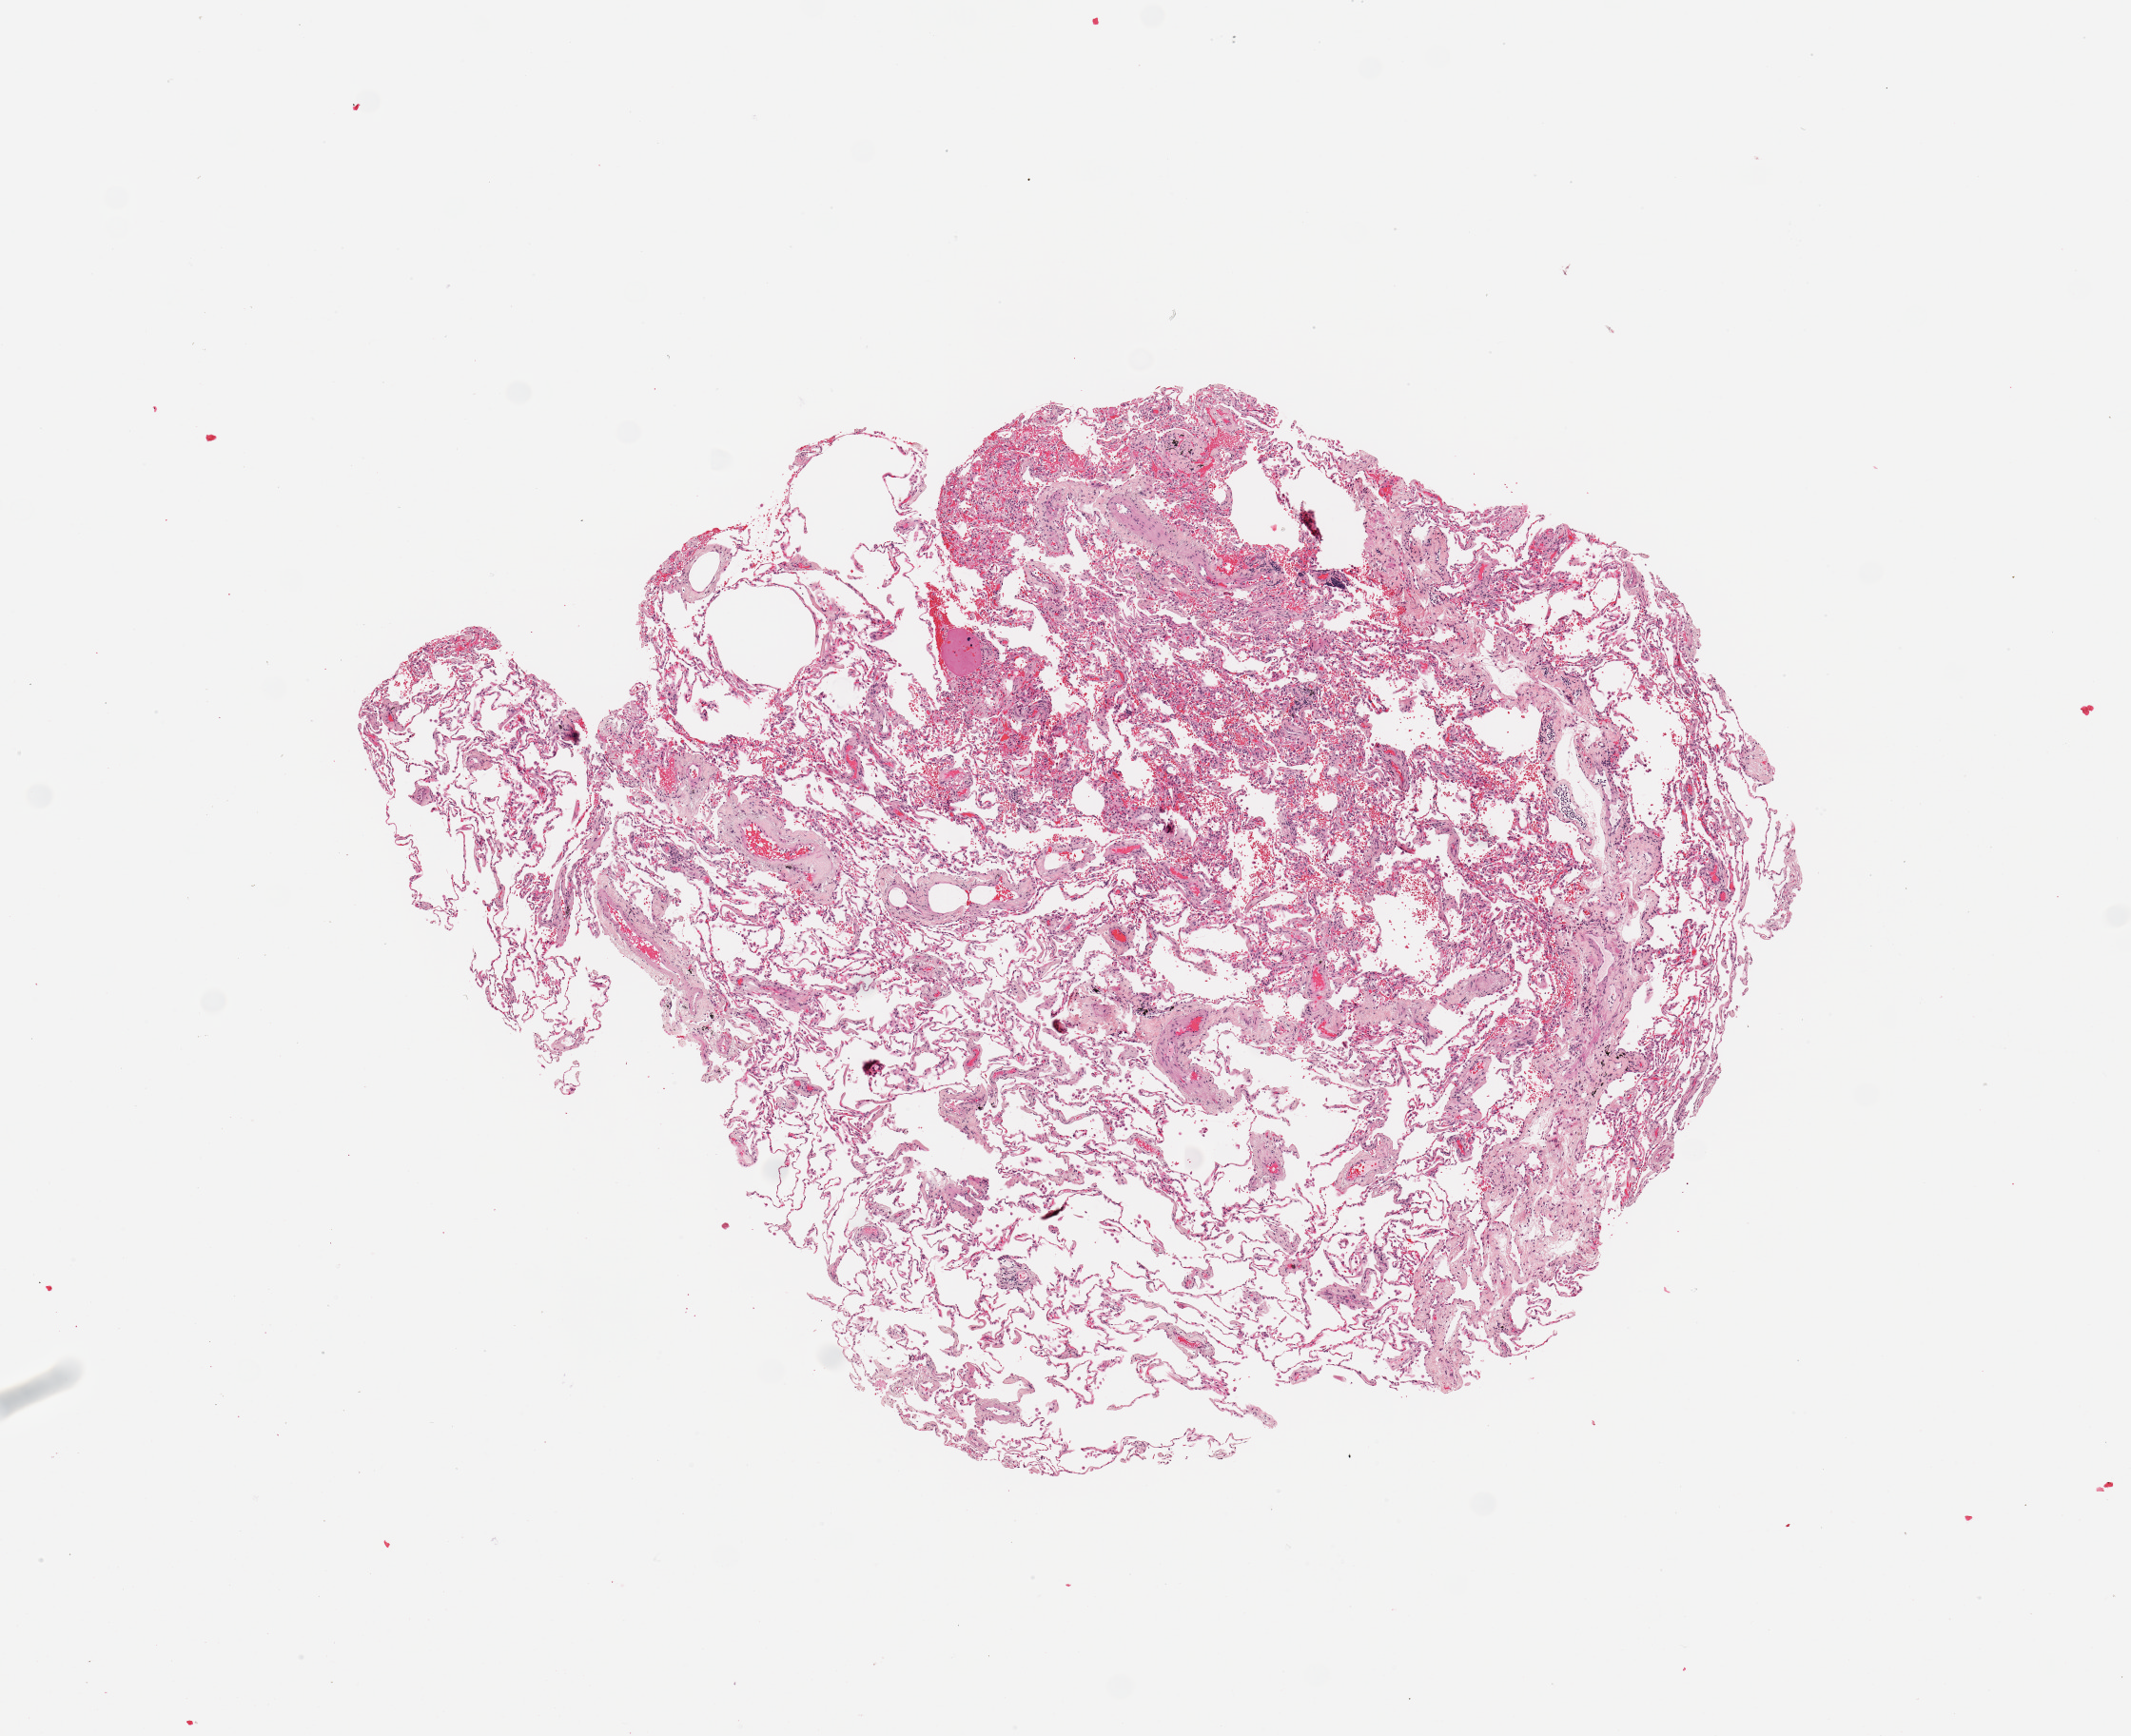
Hematoxylin and eosin (H&E) stained whole-slide image, whole scanned area (about 8.9 x 7.2 mm, from a 20x scan) shown as a low-resolution overview; normal (non-tumour) tissue sample, sampled site: lung. Male, 78 y/o.
This section: normal (non-tumour) tissue from the same patient. Patient diagnosis: Squamous cell carcinoma, NOS.